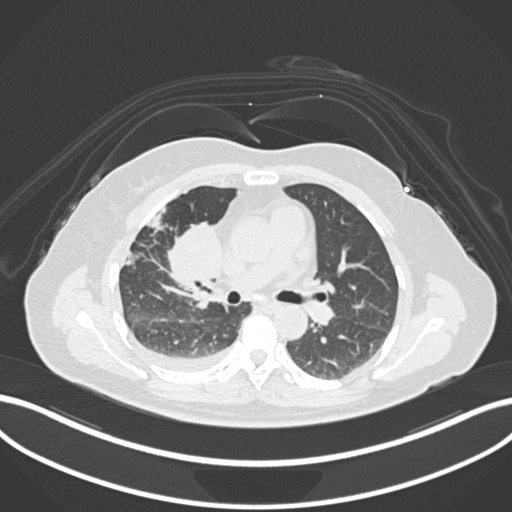
Chest CT, one axial slice; reconstruction kernel B30f; 120 kVp; lung window (W 1500 / L -600 HU); 512 × 512 image matrix, field of view 400 × 400 mm. Female patient, age 52 years. From the clinical record (not read from this slice): clinical TNM (as recorded): T3 N1 M1.
Structures marked on this image (bounding box drawn by a radiologist):
- lung tumour (recorded histology: adenocarcinoma): box from (x=165, y=211) to (x=223, y=291) px